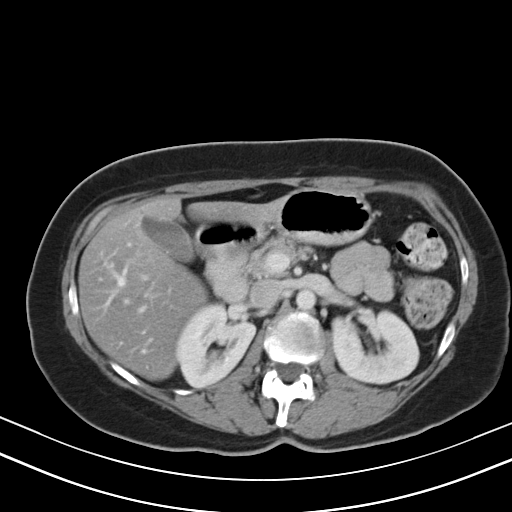
Contrast-enhanced abdominal CT, one axial slice. Position 24 of 47 along the scan axis. Reconstruction kernel B40s. 130 kVp. Intravenous contrast given. Soft-tissue window (W 400 / L 40 HU). 512 × 512 image matrix. Female patient. Case-level facts recorded for this patient, not image findings: diagnosis: colorectal cancer liver metastases, imaged before liver resection; multiple liver metastases: no; largest metastasis: 3.5 cm; chemotherapy before resection: yes.
Outlined on this slice (outlined manually by an expert reader):
- hepatic veins: bounding box [x1, y1, x2, y2] px = [106, 268, 126, 304]
- liver: [80, 198, 263, 377]
- planned liver remnant (the part of the liver to remain after resection): [80, 198, 263, 377]
- portal vein (with intrahepatic branches): [140, 274, 149, 310]